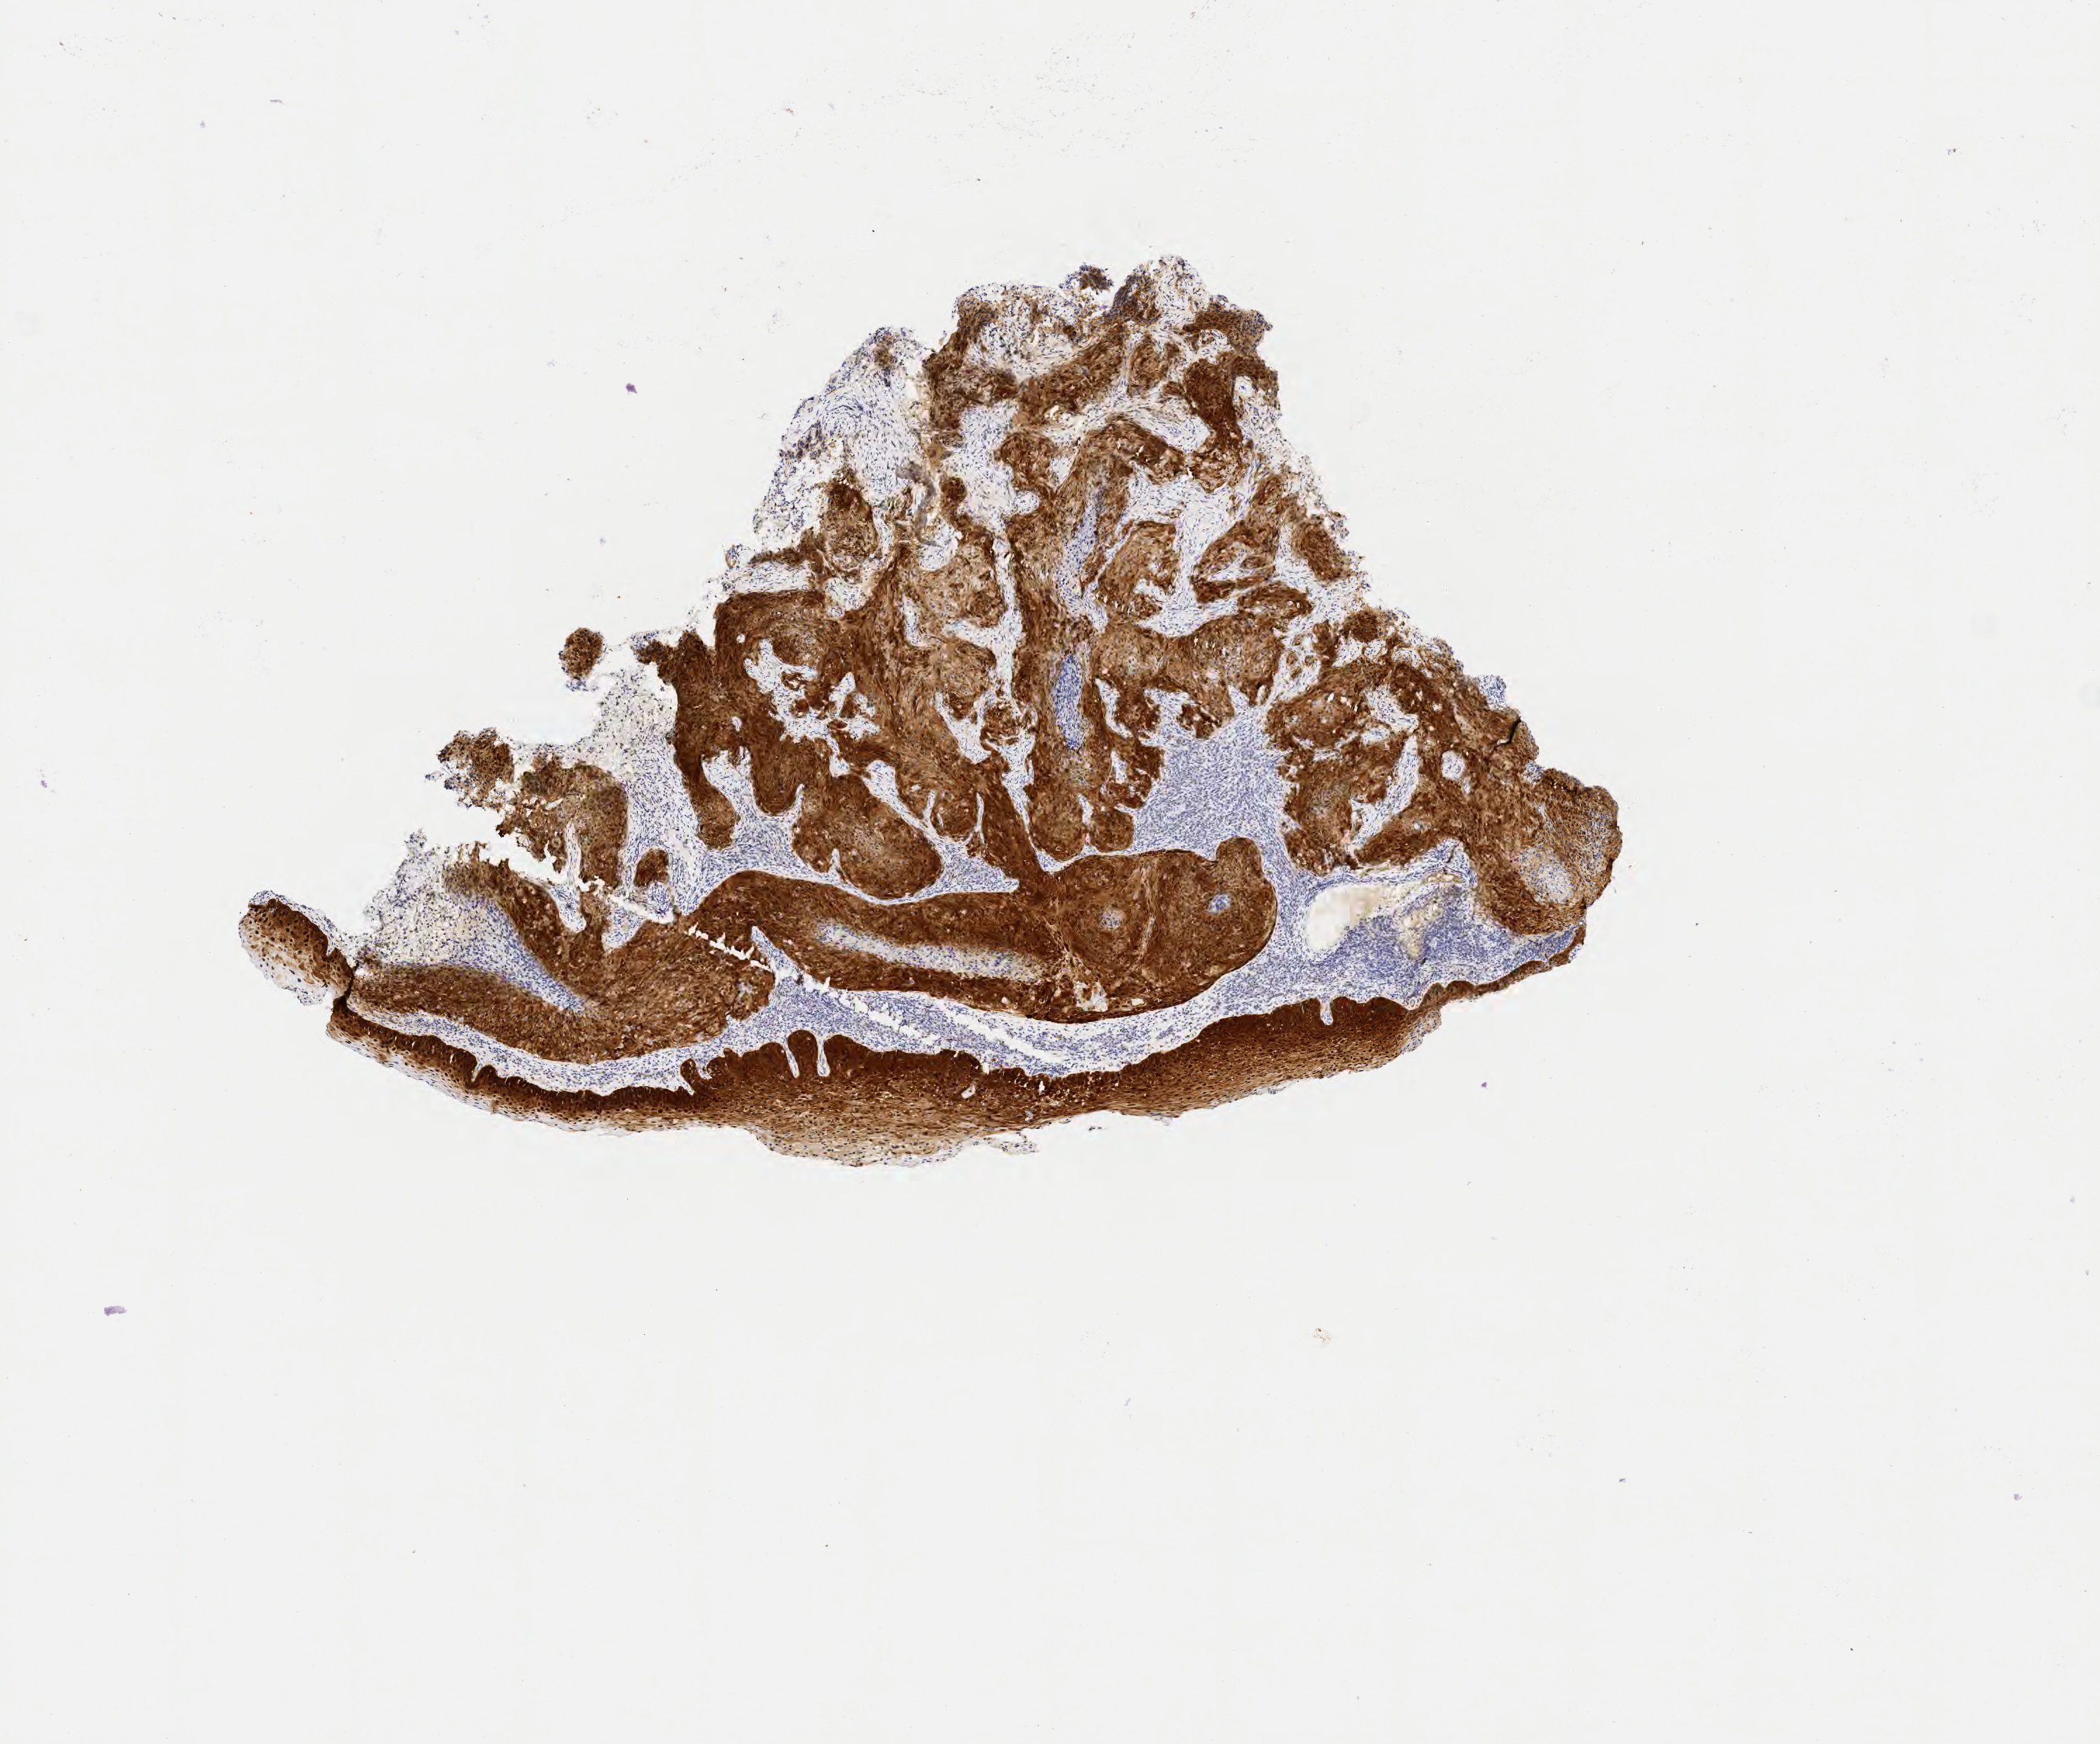
Whole-slide image, immunohistochemical stain for p16 (p16INK4a), shown as a low-resolution overview of the whole scanned area (about 6.0 x 5.0 mm); specimen: tumor tissue; site: cervix. Female patient, 36 years old.
Histologic diagnosis: Squamous cell carcinoma, large cell, nonkeratinizing, NOS.